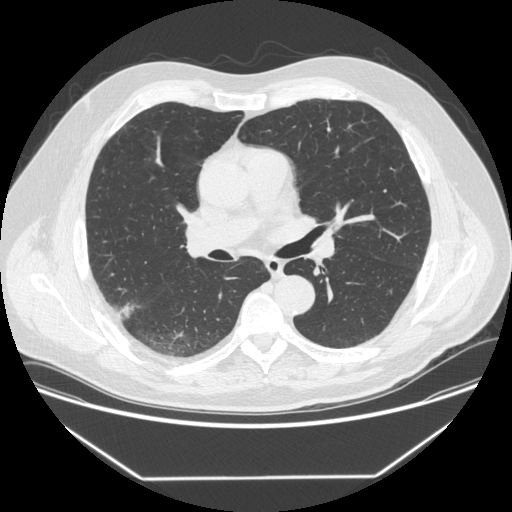
Low-dose screening chest CT, one axial slice. Position 207 of 342 along the scan axis. 120 kVp. Lung window (W 1500 / L -600 HU). 512 × 512 image matrix, field of view 410 × 410 mm.
Outlined on this slice (outlined manually by an expert reader):
- lesion 1 (tumor, upper lobe of right lung): bounding box <118,303,134,318> (left, top, right, bottom; pixels)